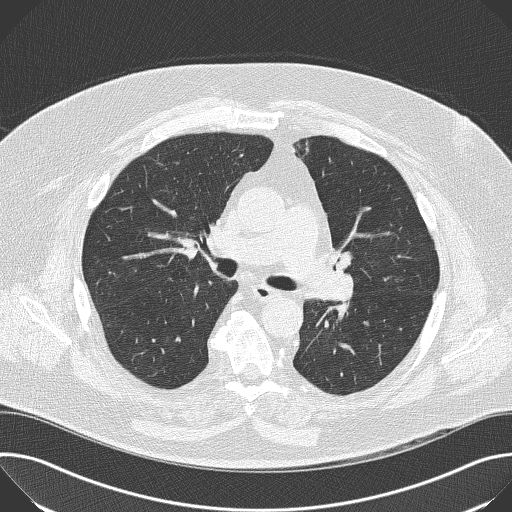
Axial slice from a low-dose chest CT screening exam, first (baseline) screen, lung window (W 1500 / L -600 HU), 512 × 512 image matrix, field of view 380 × 380 mm. Male, age 68 years at enrolment. Former smoker at enrolment.
Lesion marked by an expert reader, box from (x=318, y=235) to (x=368, y=283) px. The screening reader recorded 2 non-calcified nodules or masses ≥4 mm on this exam (left lower lobe, right lower lobe); which of them this box marks is not recorded. Official screen result: positive, change unspecified: nodule(s) >= 4 mm or enlarging nodule(s), mass(es), or other non-specific abnormalities suspicious for lung cancer. Lung cancer was diagnosed 638 days after this screen (after the second annual screen): squamous cell carcinoma, NOS, left upper lobe, poorly differentiated (G3), stage IIB (AJCC 6th edition), 35 mm at pathology.